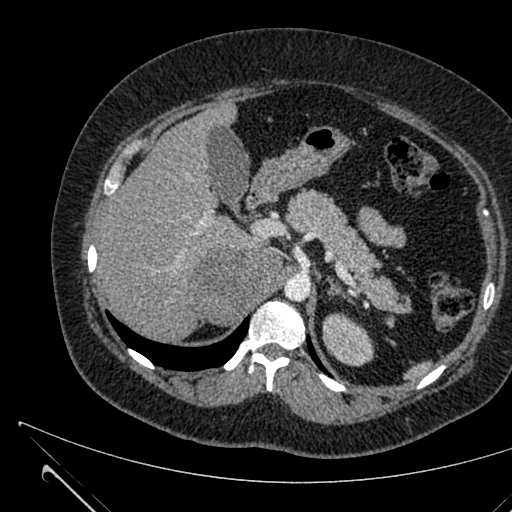
Contrast-enhanced abdominal CT, one axial slice. Slice 449 of 731 in the series (ordered by position). Intravenous contrast given. Soft-tissue window (W 400 / L 40 HU). 1 mm slice thickness. 512 × 512 image matrix. Female patient, age 36 years. From the clinical record (not read from this slice): diagnosis: adrenocortical carcinoma; tumour side: right adrenal; tumour size at pathology: 10 cm; Ki-67 index: 20 %; stage (as recorded): 4.
Annotated regions visible in this slice (semi-automatically segmented with operator editing):
- mass: bounding box <192,247,280,323> (left, top, right, bottom; pixels)